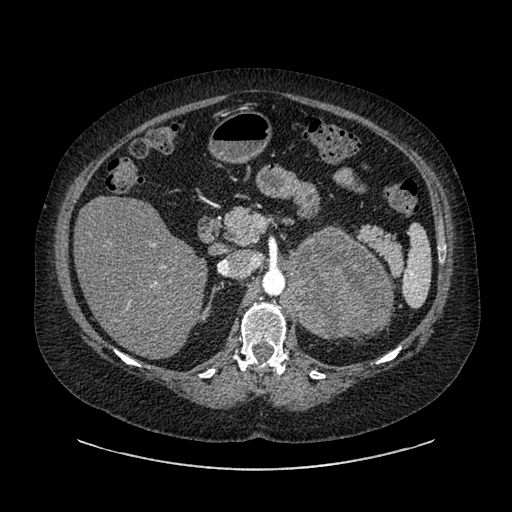
Contrast-enhanced abdominal CT, one axial slice; slice 560 of 769 in the series (ordered by position); 120 kVp; intravenous contrast given; soft-tissue window (W 400 / L 40 HU); 0.62 mm slice thickness; 512 × 512 image matrix, field of view 460 × 460 mm. Patient: female, 61 years. Case-level facts recorded for this patient, not image findings: diagnosis: adrenocortical carcinoma; tumour side: left adrenal; tumour size at pathology: 13 cm; Ki-67 index: 79 %; stage (as recorded): 2.
Structures marked on this image (semi-automatically segmented with operator editing):
- mass: box from (x=283, y=228) to (x=390, y=336) px